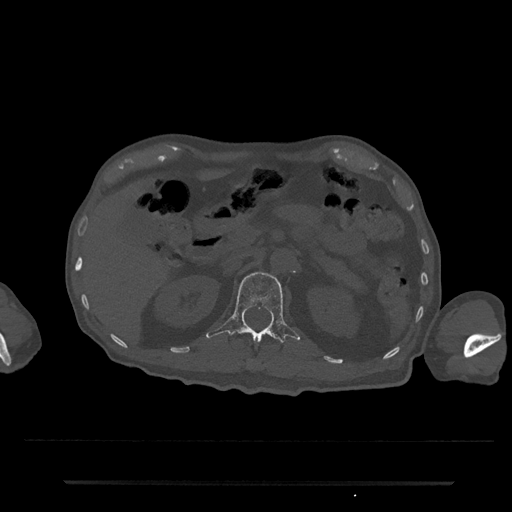
CT including the spine, one axial slice; slice 138 of 797 in the series (ordered by position); reconstruction kernel Br40s/3; 120 kVp; bone window (W 1800 / L 400 HU); 0.5 mm slice thickness; 512 × 512 image matrix, field of view 427 × 427 mm. Male patient, age 74 years. From the clinical record (not read from this slice): primary cancer: prostate.
Outlined on this slice (semi-automatic segmentation, software-assisted and operator-edited):
- L1 vertebra: bounding box (x1, y1, x2, y2) in pixels: (206, 272, 300, 343)
- T12 vertebra: (250, 364, 252, 366)